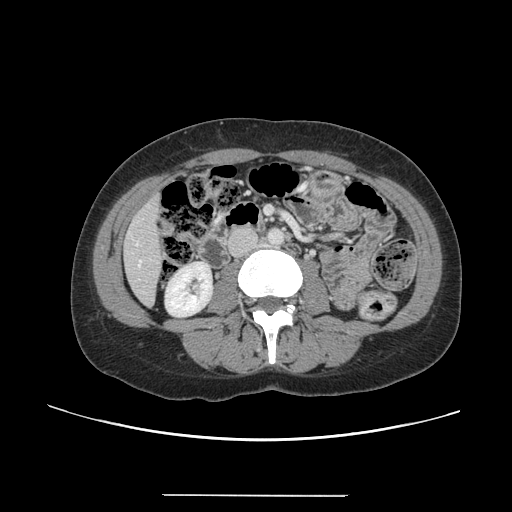
Contrast-enhanced abdominal CT, one axial slice; position 34 of 144 along the scan axis; 120 kVp; soft-tissue window (W 400 / L 40 HU); 512 × 512 image matrix. Female patient, age 53 years. From the clinical record (not read from this slice): diagnosis: colorectal cancer liver metastases, imaged before liver resection; multiple liver metastases: yes; largest metastasis: 1.1 cm; disease in both lobes: no.
Outlined on this slice (manually delineated by an expert):
- hepatic veins: box from (x=139, y=260) to (x=141, y=265) px
- liver: (x=125, y=199)–(x=164, y=304)
- planned liver remnant (the part of the liver to remain after resection): (x=125, y=196)–(x=164, y=305)